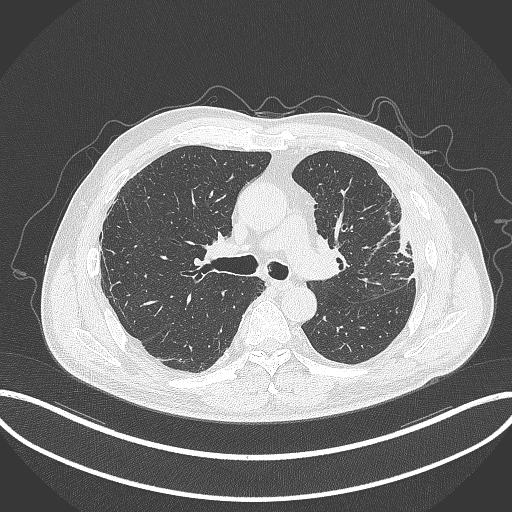
Chest CT, one axial slice. Slice 215 of 382 in the series (ordered by position). 120 kVp. Lung window (W 1500 / L -600 HU). 1 mm slice thickness. 512 × 512 image matrix, field of view 415 × 415 mm. Patient: male, 64 years. Case-level facts recorded for this patient, not image findings: clinical TNM (as recorded): T4 N1 M0; histopathological grade: G3.
Structures marked on this image (bounding box drawn by a radiologist):
- lung tumour (recorded histology: adenocarcinoma): bounding box (x1, y1, x2, y2) in pixels: (387, 209, 416, 265)